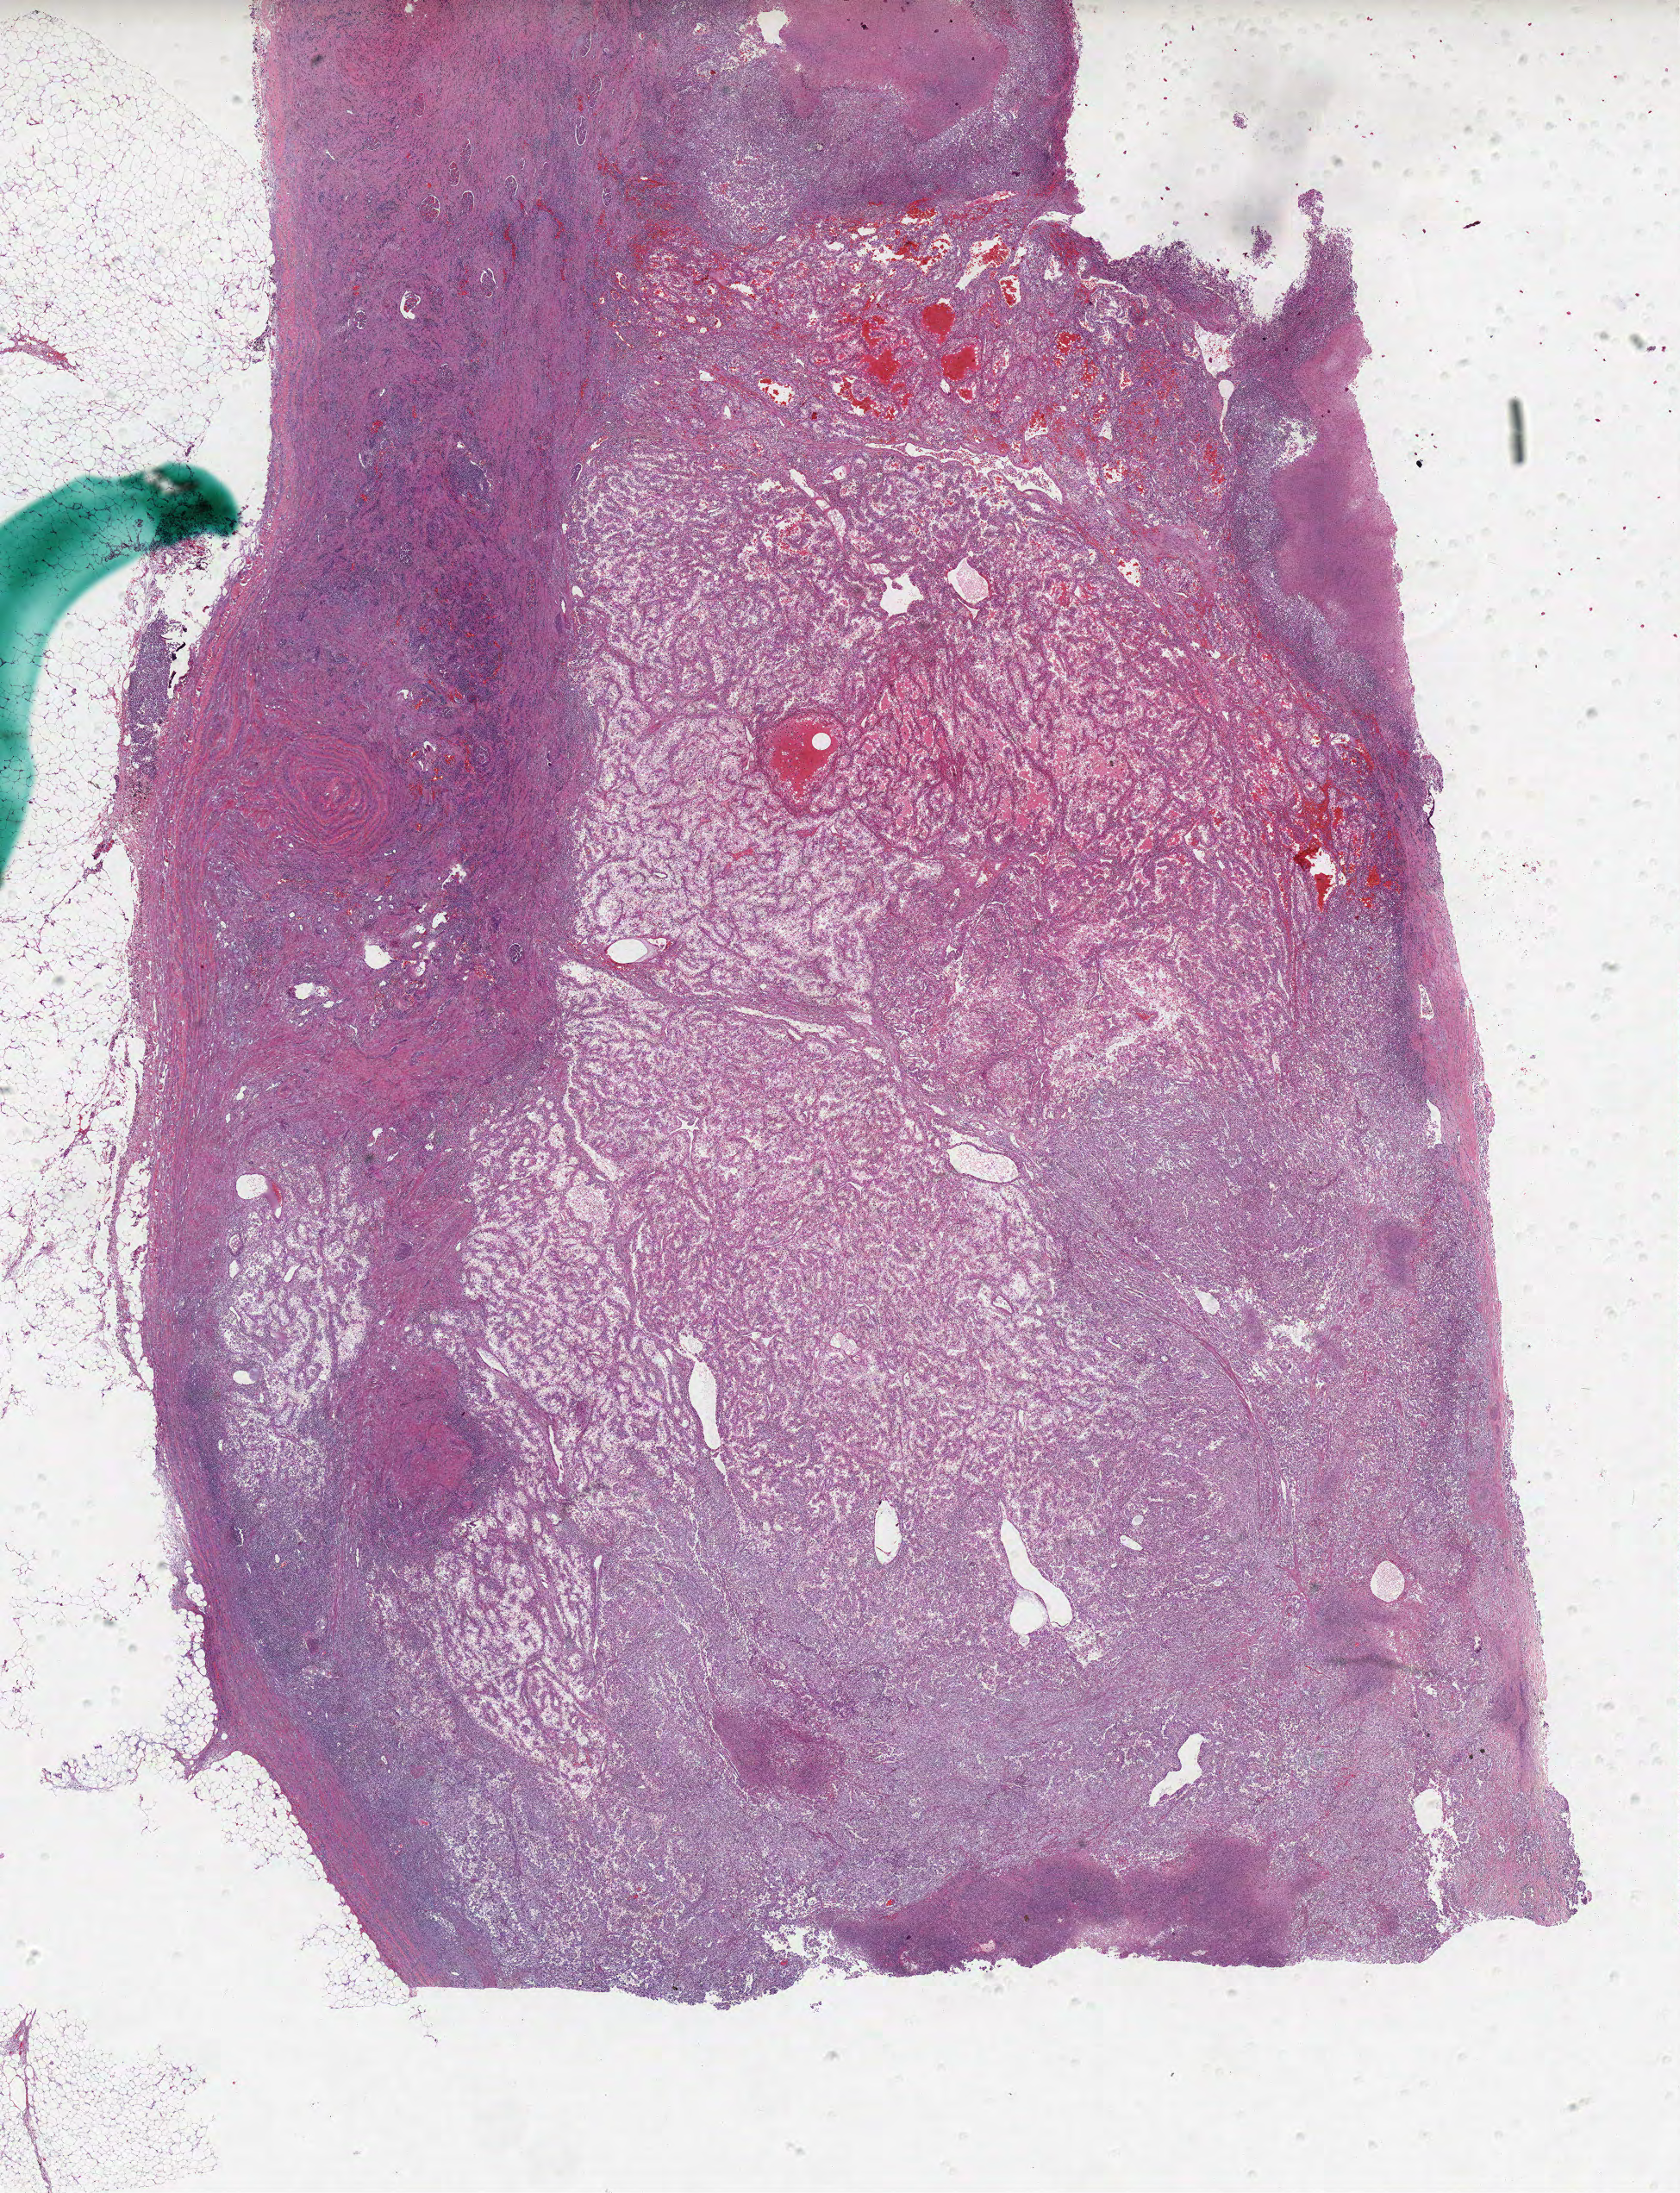
Digitized H&E tissue section (whole slide), shown as a low-resolution overview of the whole scanned area (about 15.6 x 20.3 mm); formalin-fixed paraffin-embedded (FFPE) diagnostic section; primary tumour sample from the kidney. Male, age 62 years at initial diagnosis. Histologic grade: G4 (undifferentiated).
- lymph nodes positive (case pathology): 0 of 5 examined
- histologic diagnosis: Clear cell adenocarcinoma, NOS
- AJCC pathologic stage: IV